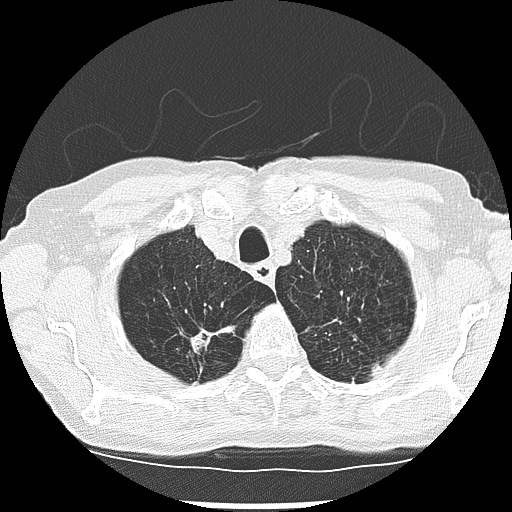
Low-dose screening chest CT, one axial slice; slice 234 of 265 in the series (ordered by position); reconstruction kernel LUNG; 120 kVp; lung window (W 1500 / L -600 HU); 2.5 mm slice thickness; 512 × 512 image matrix, field of view 300 × 300 mm.
Annotated regions visible in this slice (outlined manually by an expert reader):
- lesion 2 (tumor, upper lobe of right lung): bounding box (x1, y1, x2, y2) in pixels: (190, 329, 214, 352)